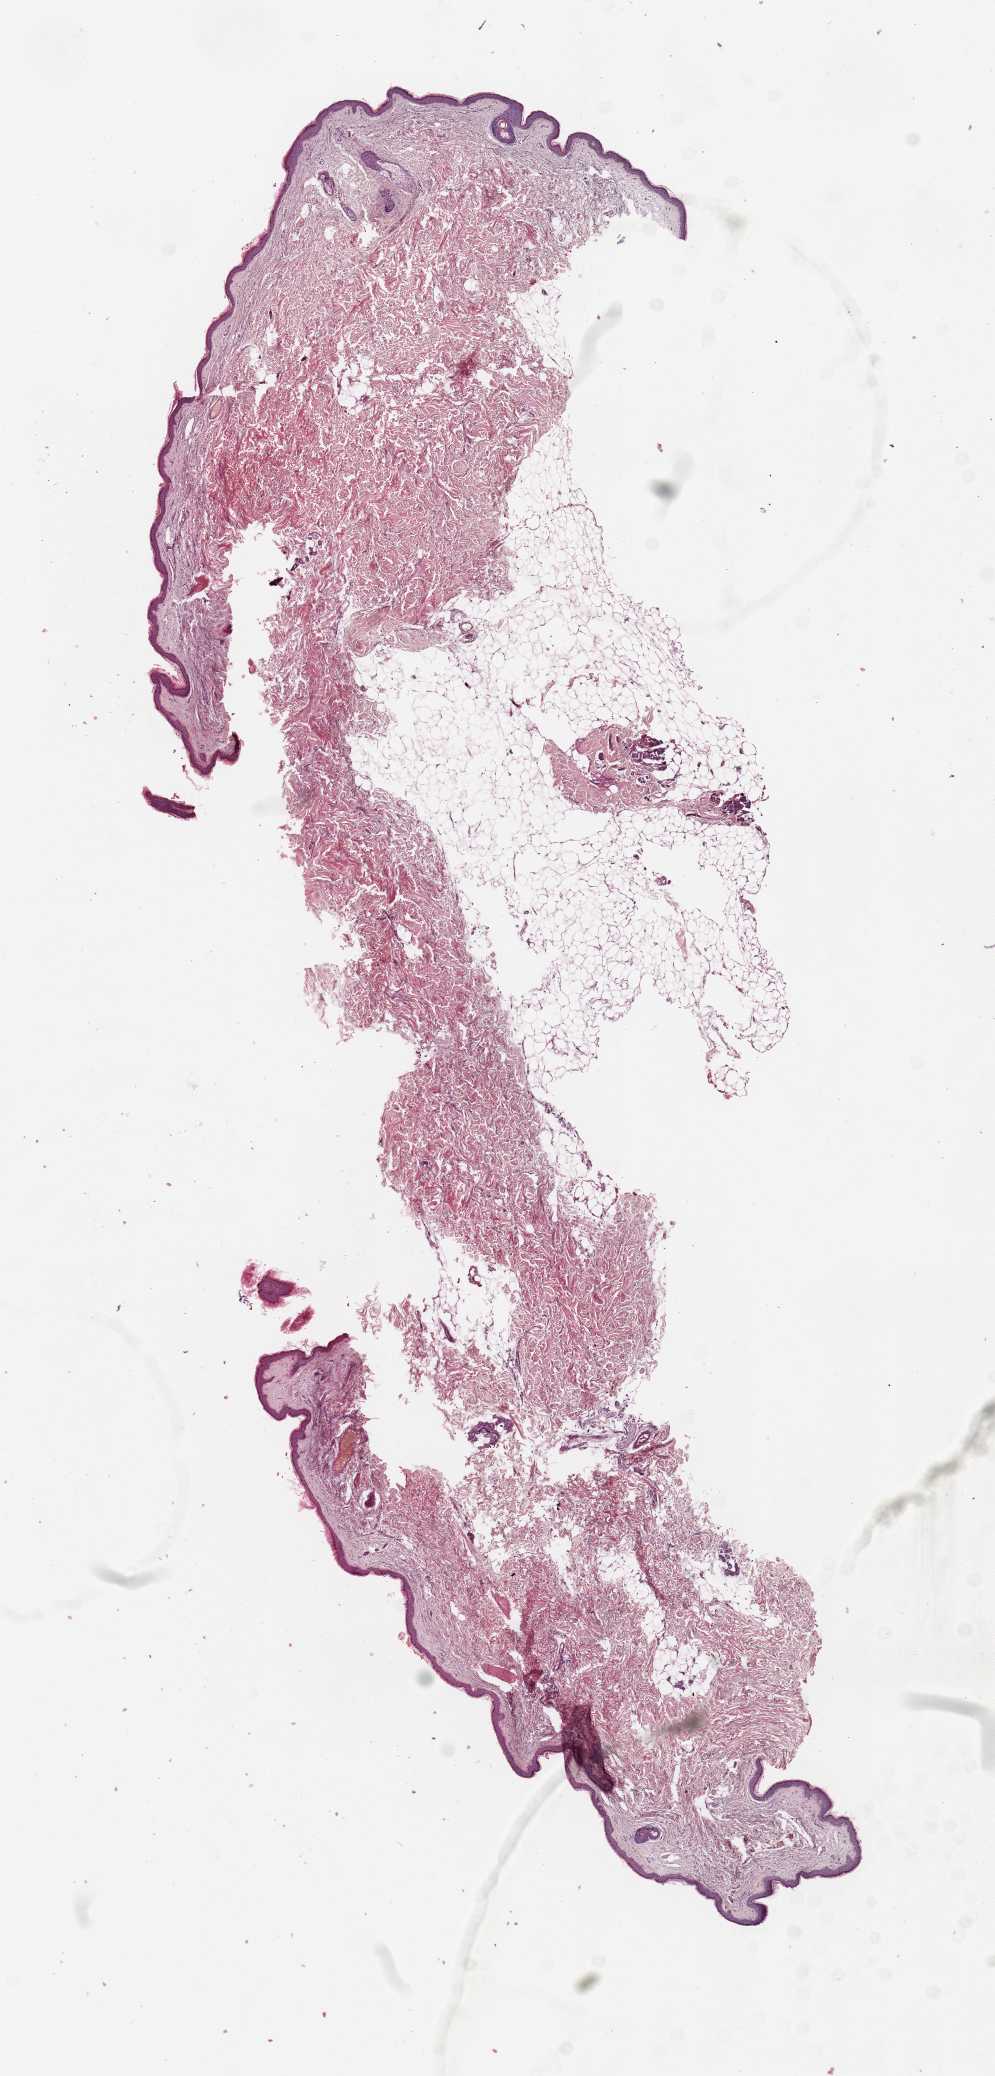
Whole-slide histology image, Hematoxylin and eosin (H&E) stained, shown as a low-resolution overview of the whole scanned area (about 7.9 x 16.4 mm, acquisition: 20x scan); normal (non-tumour) tissue sample, sampled site: lymph node. Male, 76 y/o.
This section: normal (non-tumour) tissue from the same patient. Patient diagnosis: Malignant melanoma, NOS.